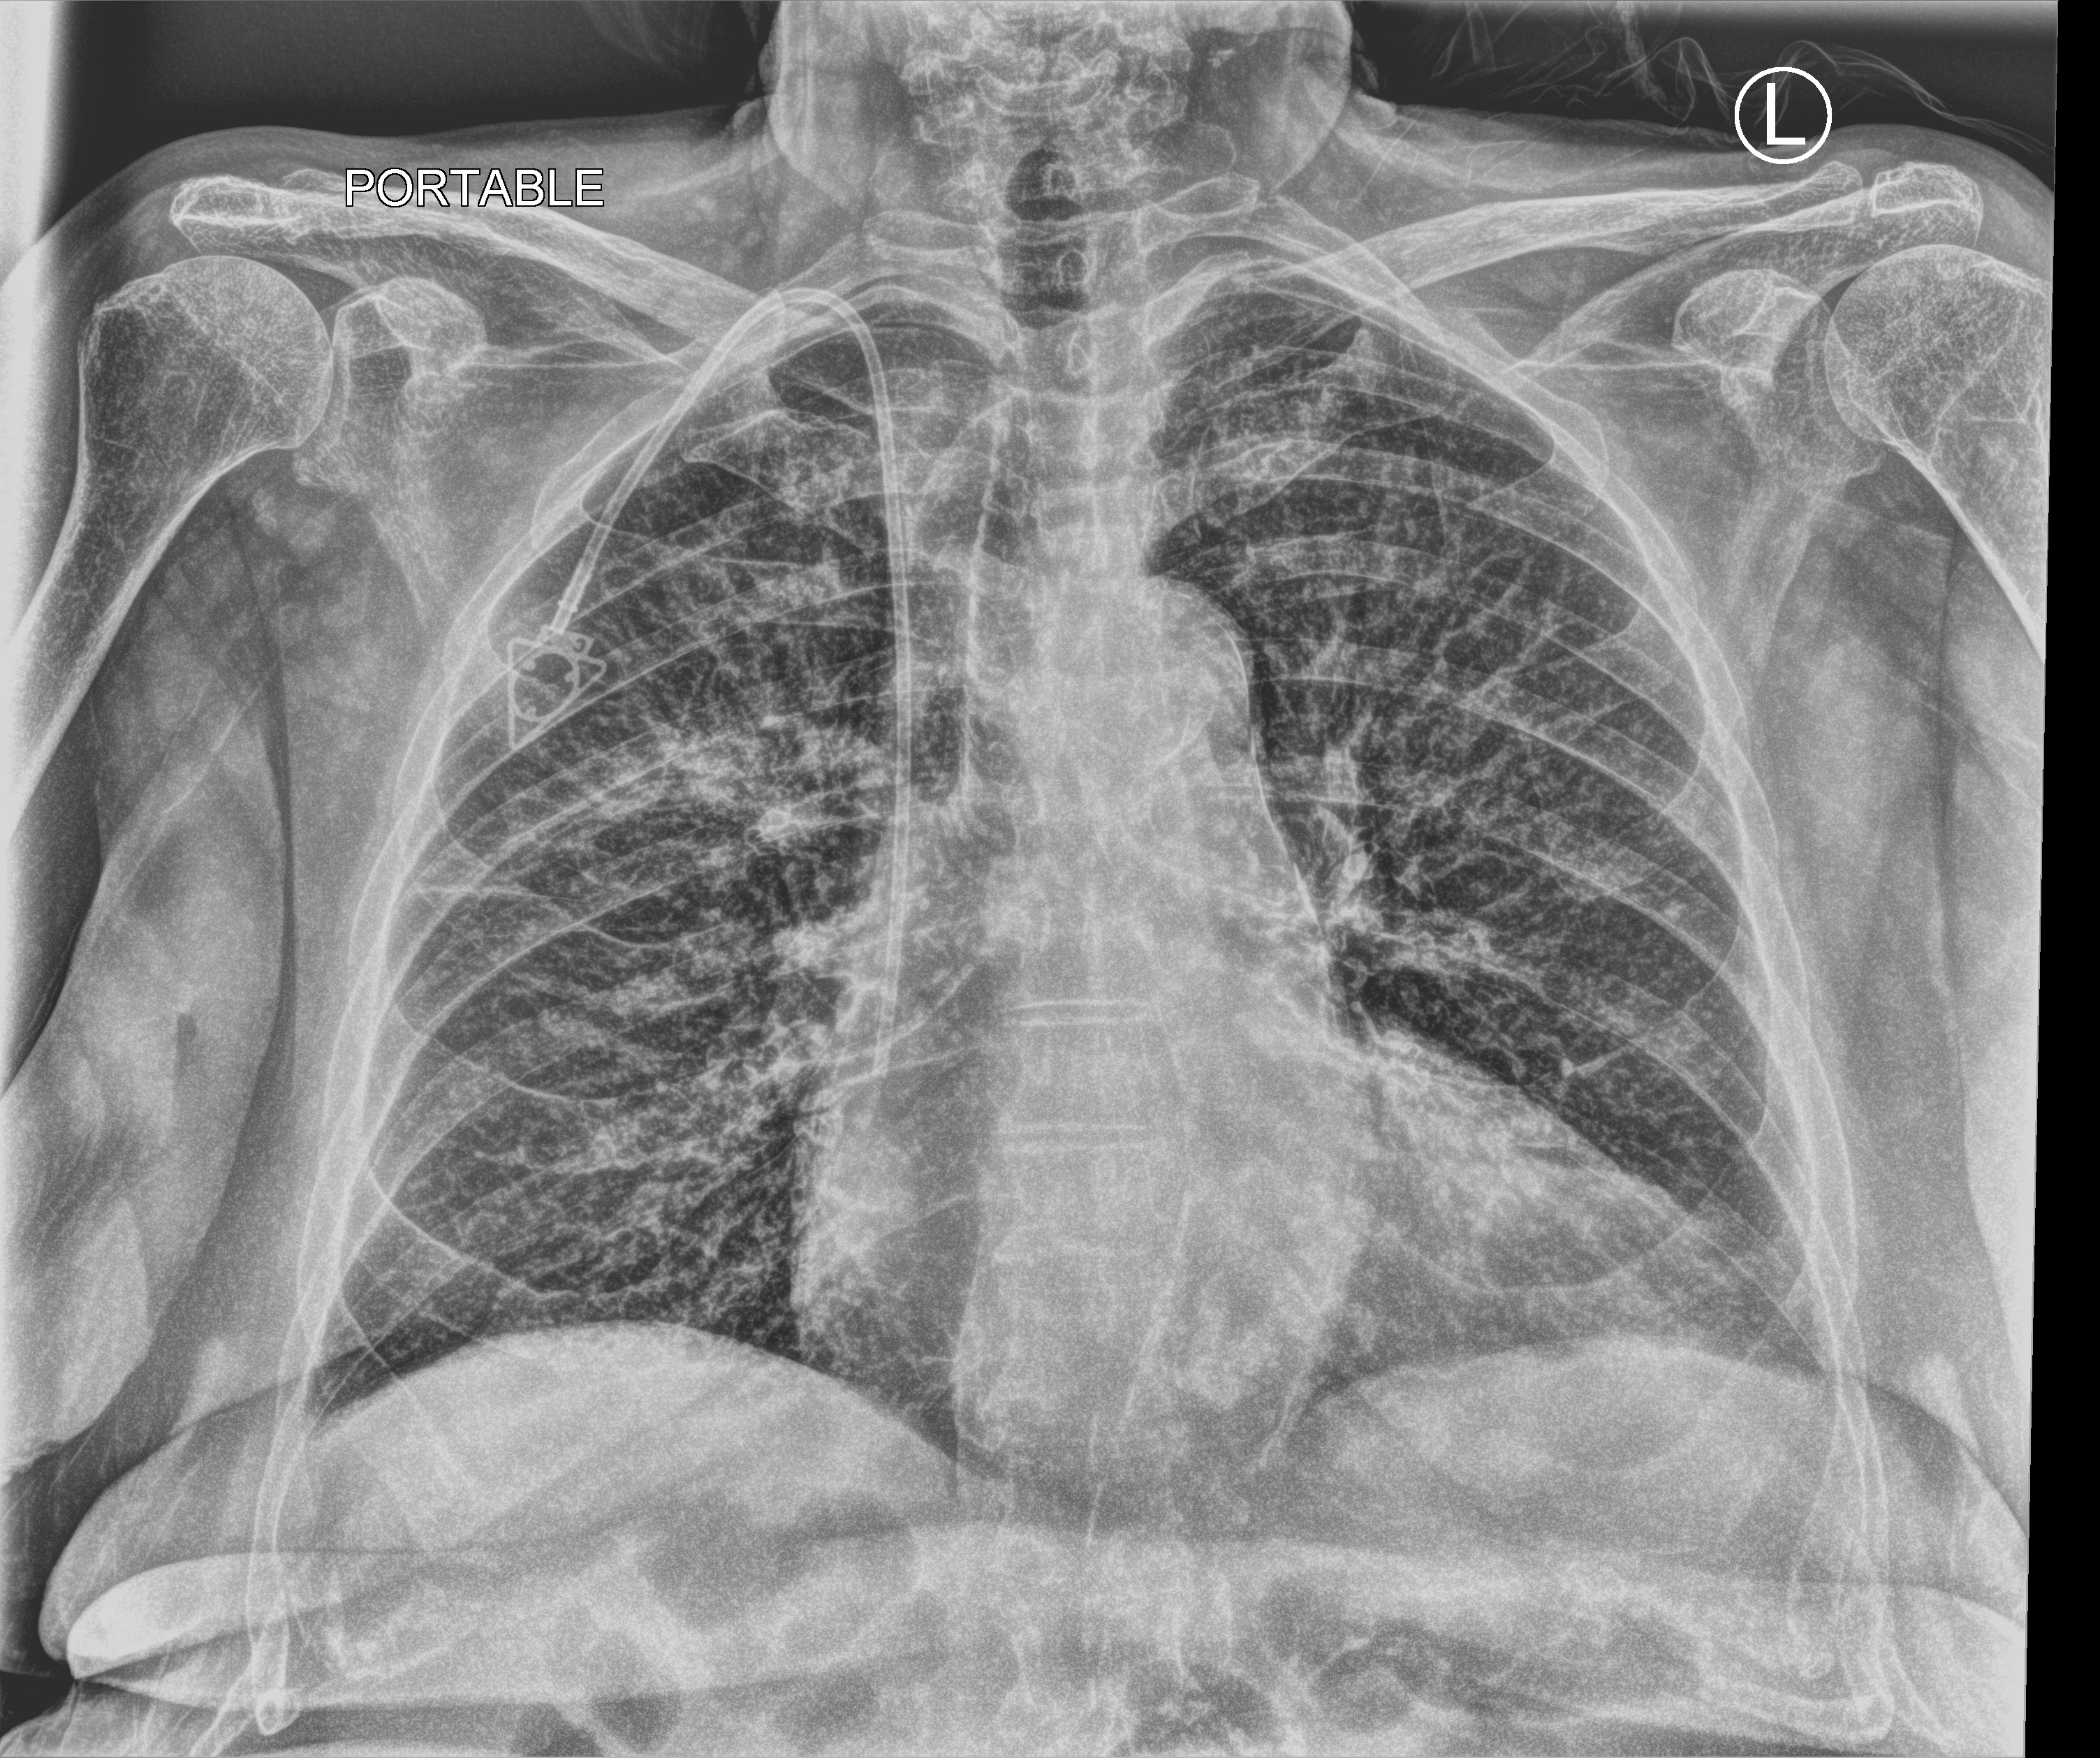
Chest X-ray (portable); anteroposterior (AP) projection. Female patient hospitalised with COVID-19, age 75–90 years.
Admission-level facts for this patient (not findings on this image; timing relative to this image not recorded): length of hospital stay: 16 days; mechanically ventilated during this hospital stay: no.